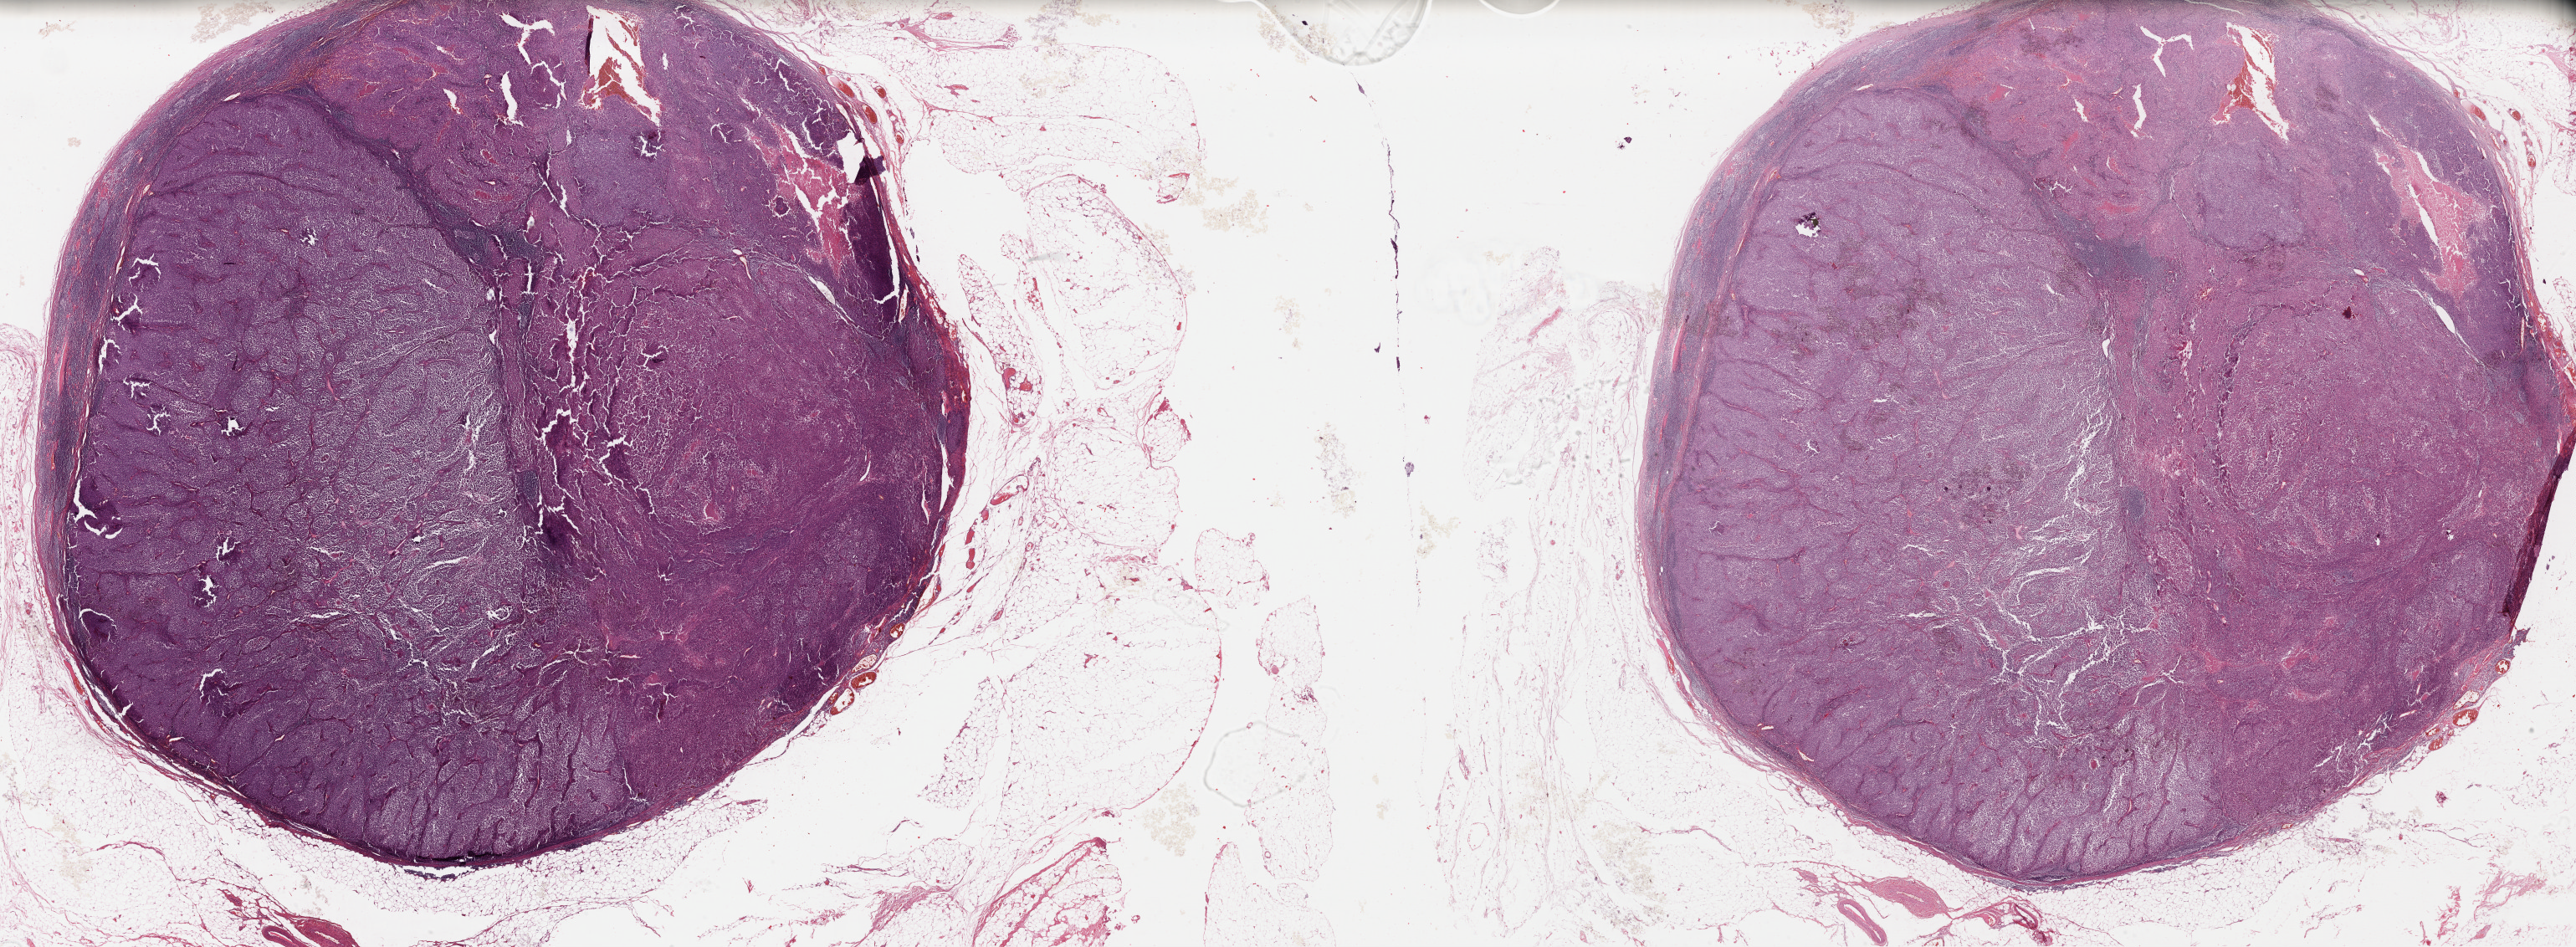
Whole-slide histology image, H&E — shown as a low-resolution overview of the whole scanned area (about 48.4 x 17.8 mm, from a 40x scan), FFPE section, metastatic tumour sample, sampled site: lymph node. Male patient; age at initial diagnosis 65 years.
This section: metastatic tumour tissue. Patient diagnosis: Malignant melanoma, NOS.